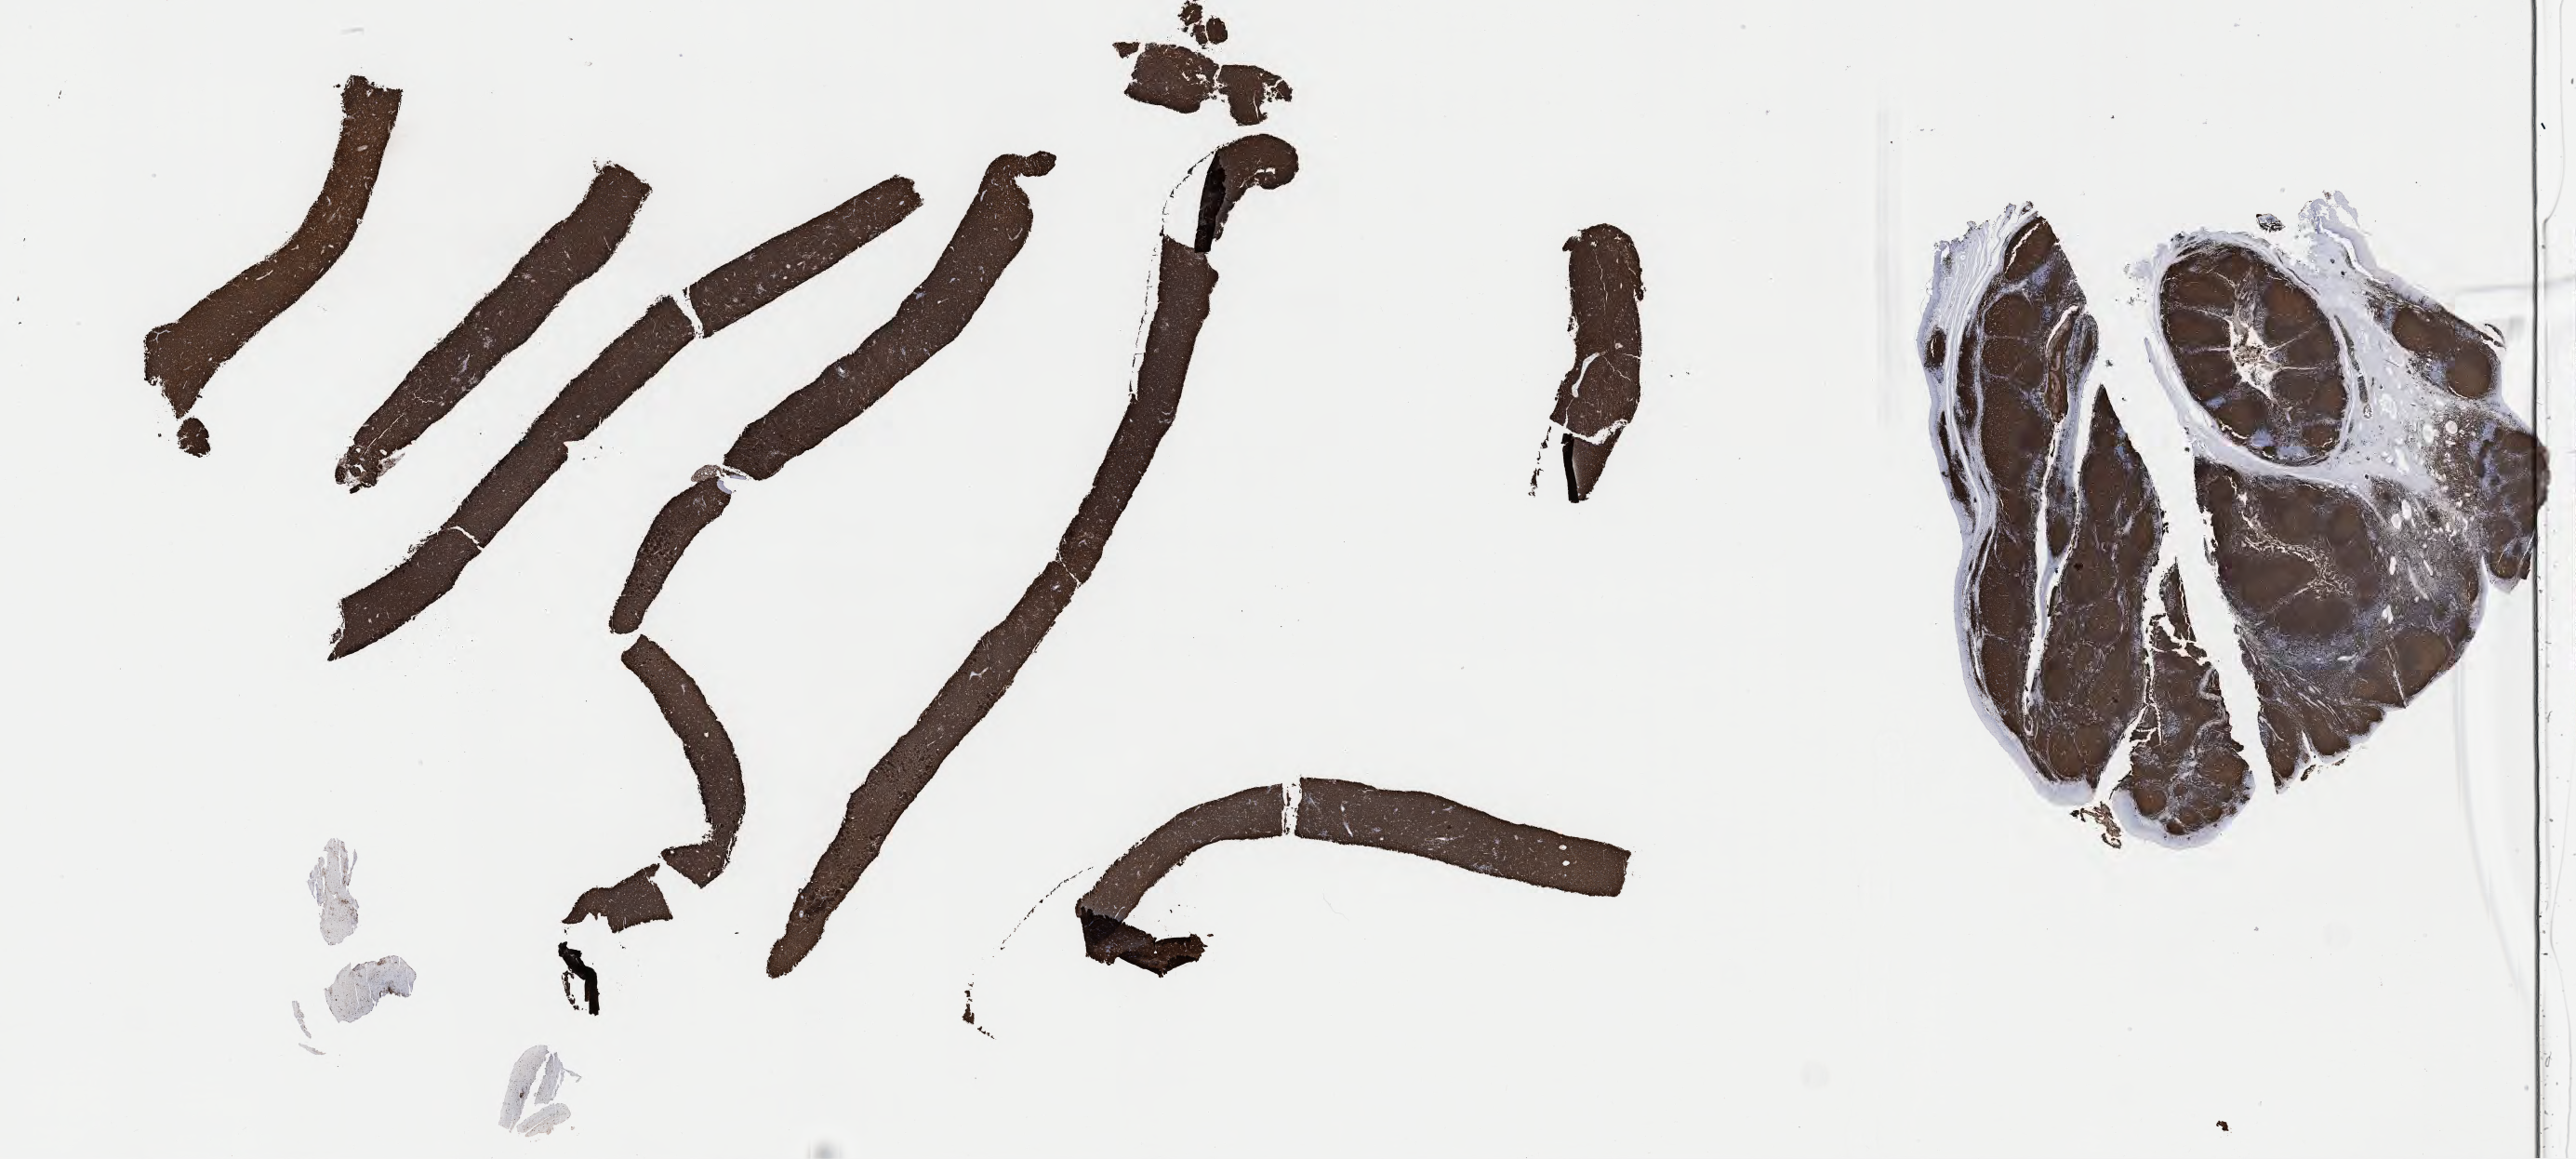
Immunohistochemistry (IHC) whole-slide image stained for CD20, whole scanned area (about 44.8 x 20.2 mm) shown as a low-resolution overview; tumor tissue. Patient male; age 29 years.
* diagnosis: Burkitt lymphoma, NOS